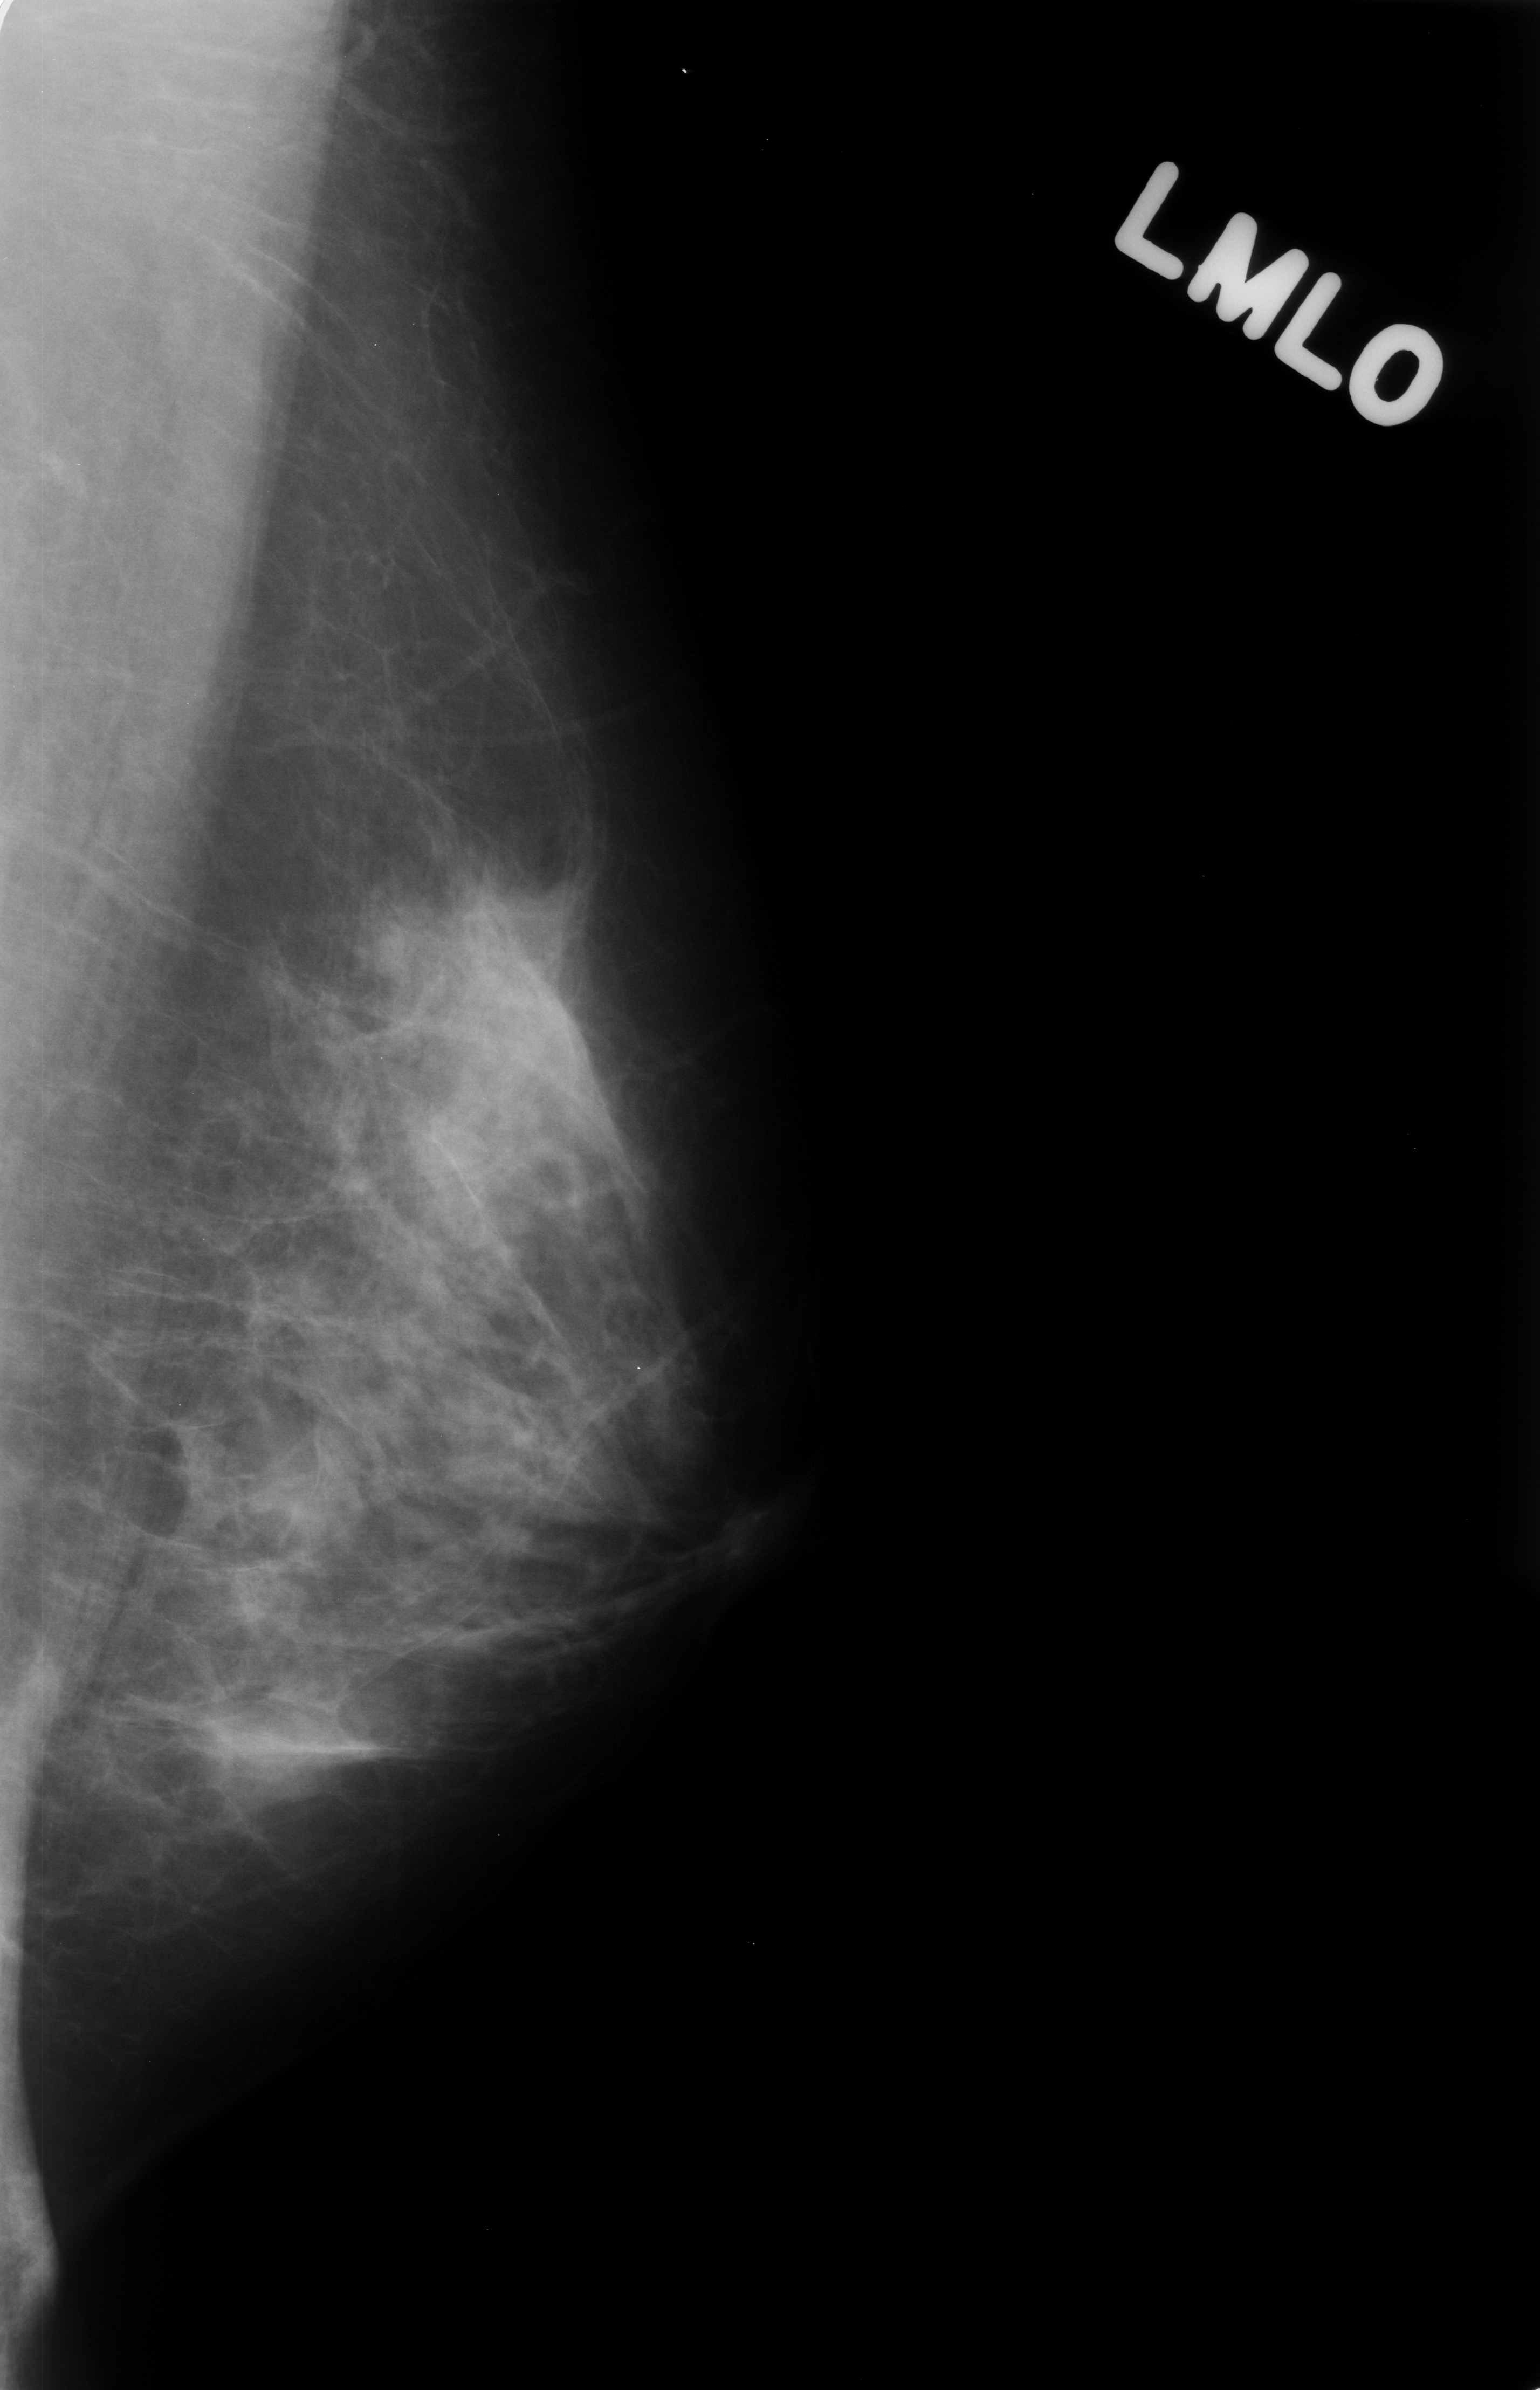
Digitized screen-film mammogram; left breast; MLO view; 1540 × 2390 image matrix.
Expert-marked regions of interest on this film, with their recorded descriptors:
- mass, shape oval, margins ill defined; BI-RADS assessment category 4; pathology result (as recorded, not read from the image): benign: box from (x=193, y=1675) to (x=405, y=1821) px